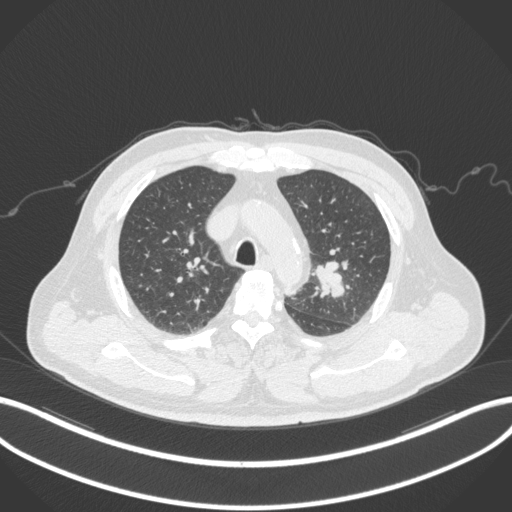
Chest CT, one axial slice; slice 227 of 286 in the series (ordered by position); reconstruction kernel B31f; lung window (W 1500 / L -600 HU); 512 × 512 image matrix, field of view 400 × 400 mm. Patient: male, 67 years. From the clinical record (not read from this slice): clinical TNM (as recorded): T2a N1 M0; histopathological grade: G3.
Outlined on this slice (rectangle marked by the reading radiologist):
- lung tumour (recorded histology: adenocarcinoma): bounding box <310,258,351,302> (left, top, right, bottom; pixels)